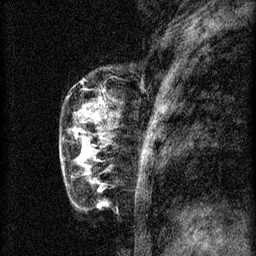
Breast MRI (dynamic contrast-enhanced), one sagittal slice; position 21 of 60 along the scan axis; 3 images stored at this slice position (order not interpretable as contrast timing); 1.5 T; TE 4.2 ms, TR 8.2 ms; 2 mm slice thickness; 256 × 256 image matrix, field of view 180 × 180 mm. Patient: female, 56 years.
Annotated regions visible in this slice (semi-automatically segmented with operator editing):
- analysis volume of interest (the breast-tissue region the enhancement analysis was run in; not a lesion): bounding box <60,124,114,179> (left, top, right, bottom; pixels)
- tumour enhancement mask (voxels above the 70 % enhancement threshold inside the analysis volume of interest): <84,150,88,153>